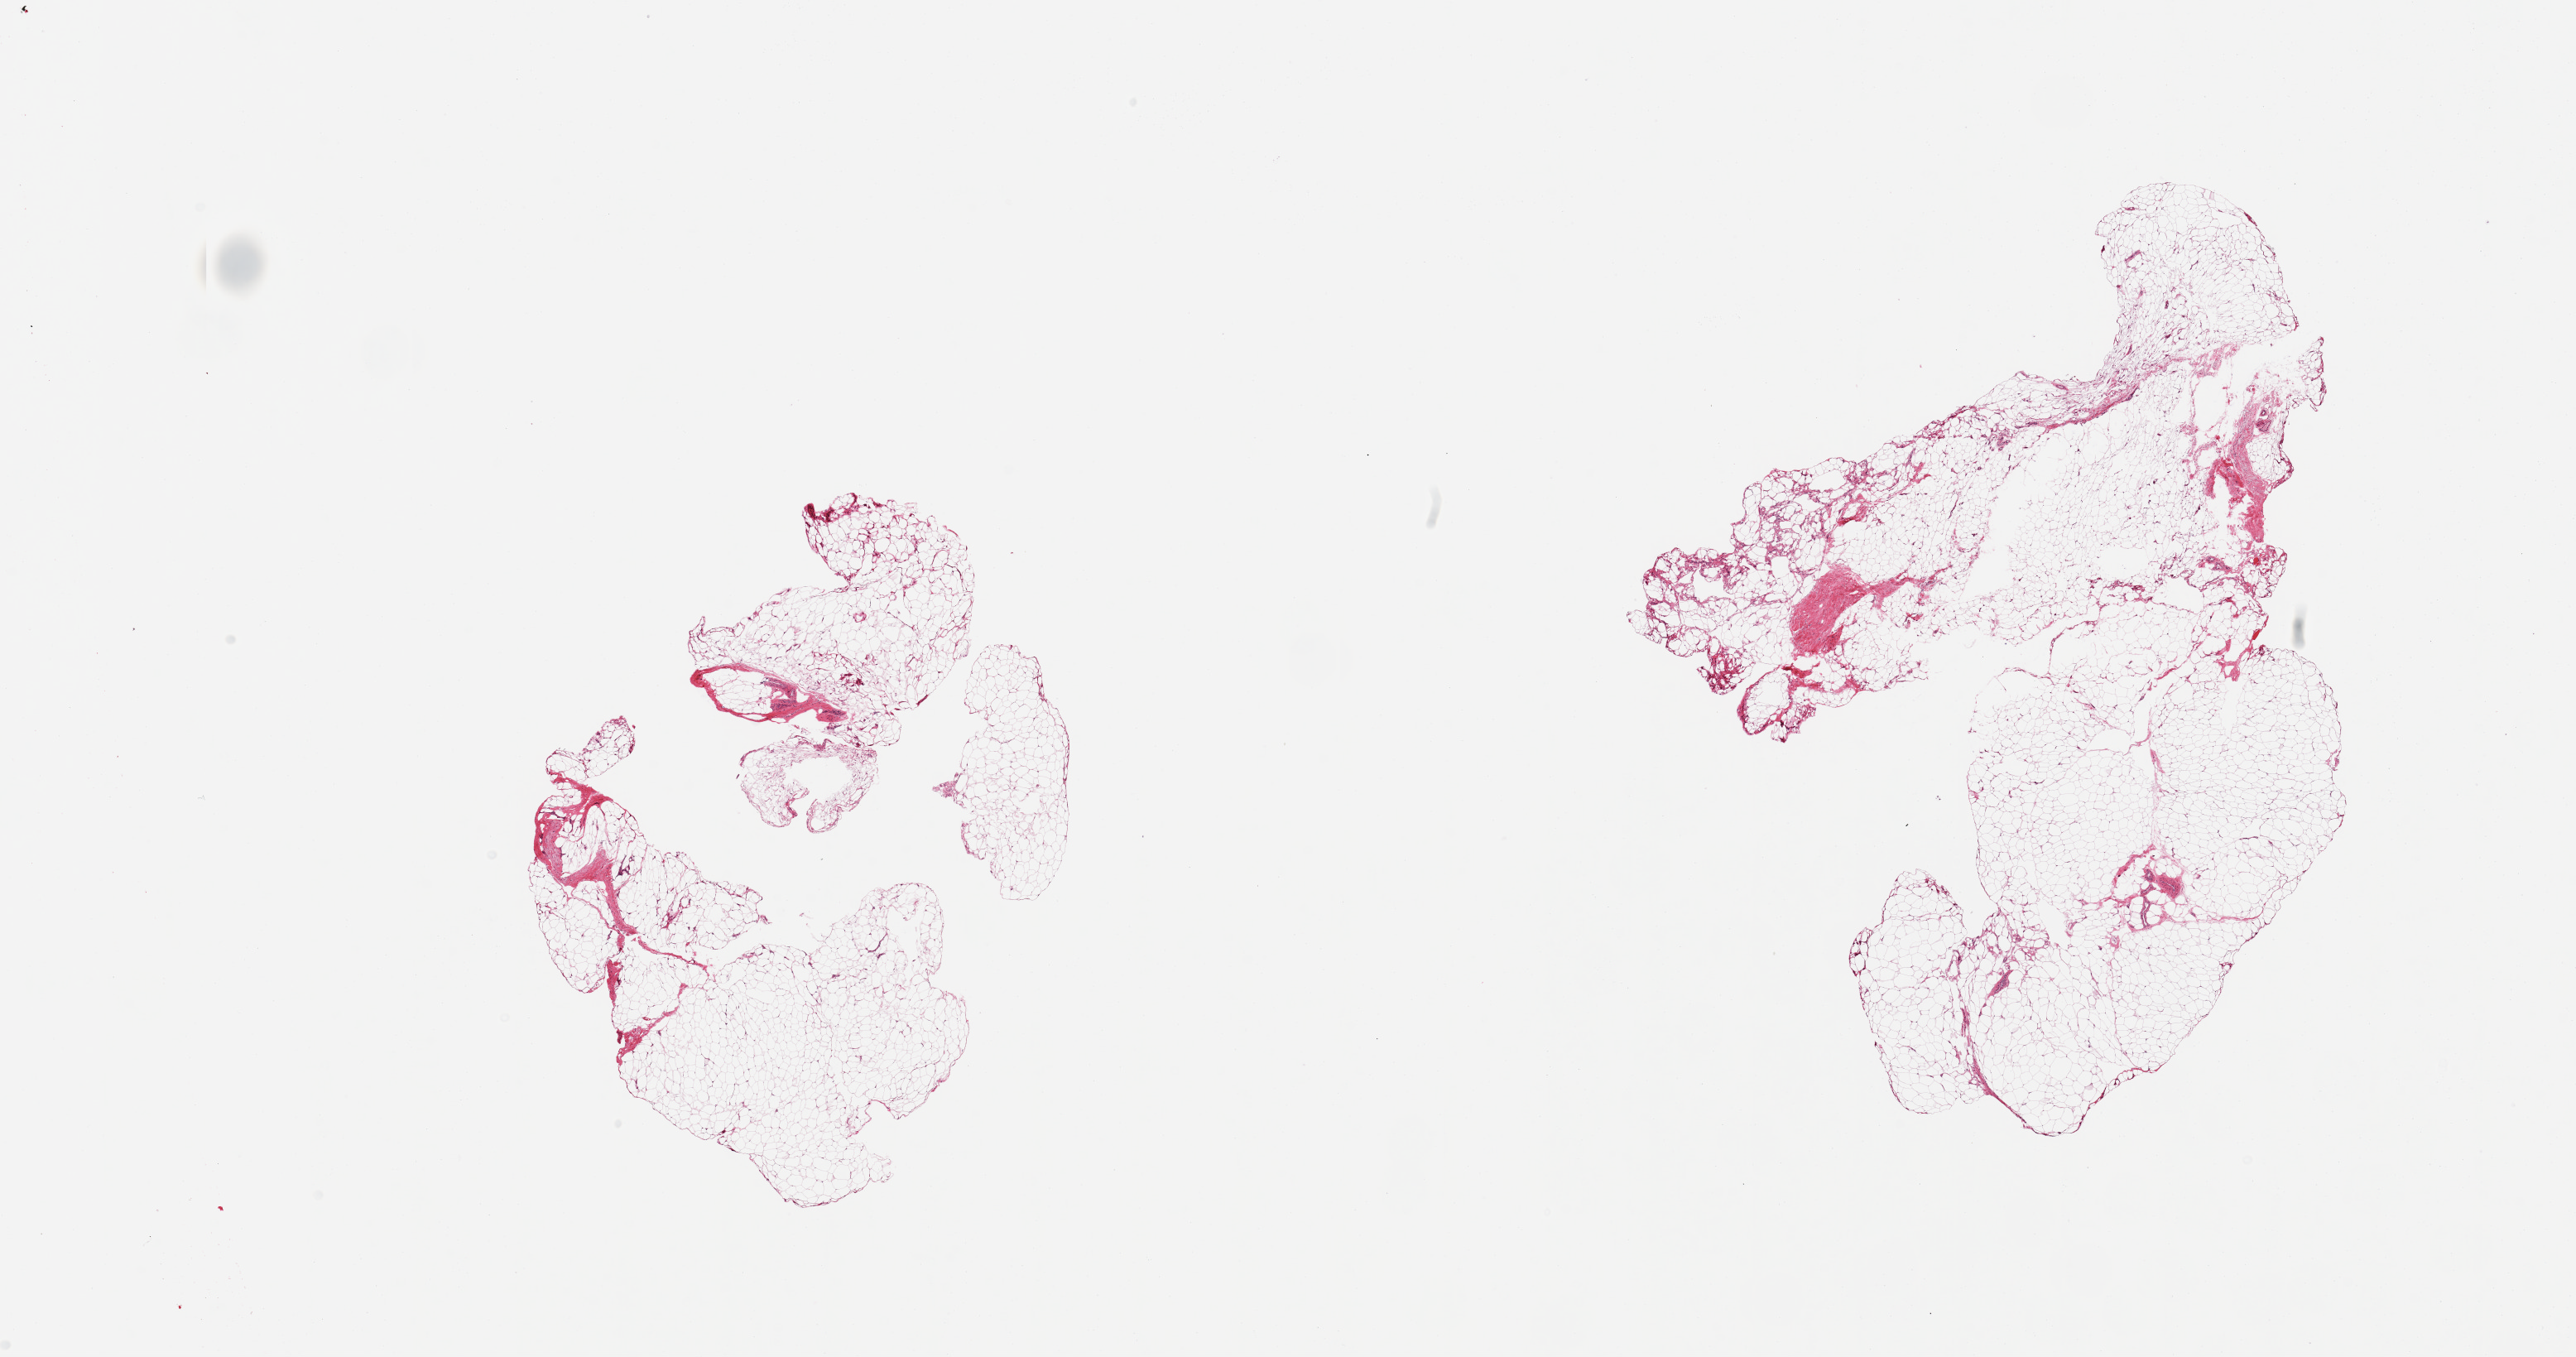
Haematoxylin and eosin whole-slide image — whole scanned area (about 24.6 x 13.0 mm) shown as a low-resolution overview, PAXgene-fixed paraffin-embedded (PFPE) section, target tissue: adipose tissue, tissue donor sample.
Review note (as recorded): 2 pieces; fat with trivial fibrous/vascular component.